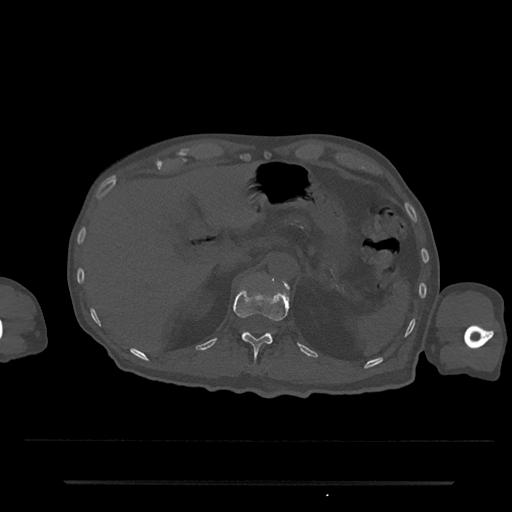
CT including the spine, one axial slice; slice 184 of 797 in the series (ordered by position); reconstruction kernel Br40s/3; 120 kVp; bone window (W 1800 / L 400 HU); 0.5 mm slice thickness; 512 × 512 image matrix. Patient: male, 74 years. From the clinical record (not read from this slice): primary cancer: prostate.
Annotated regions visible in this slice (semi-automatically segmented with operator editing):
- L1 vertebra: bounding box [x1, y1, x2, y2] px = [285, 283, 288, 287]
- T12 vertebra: [234, 287, 289, 358]